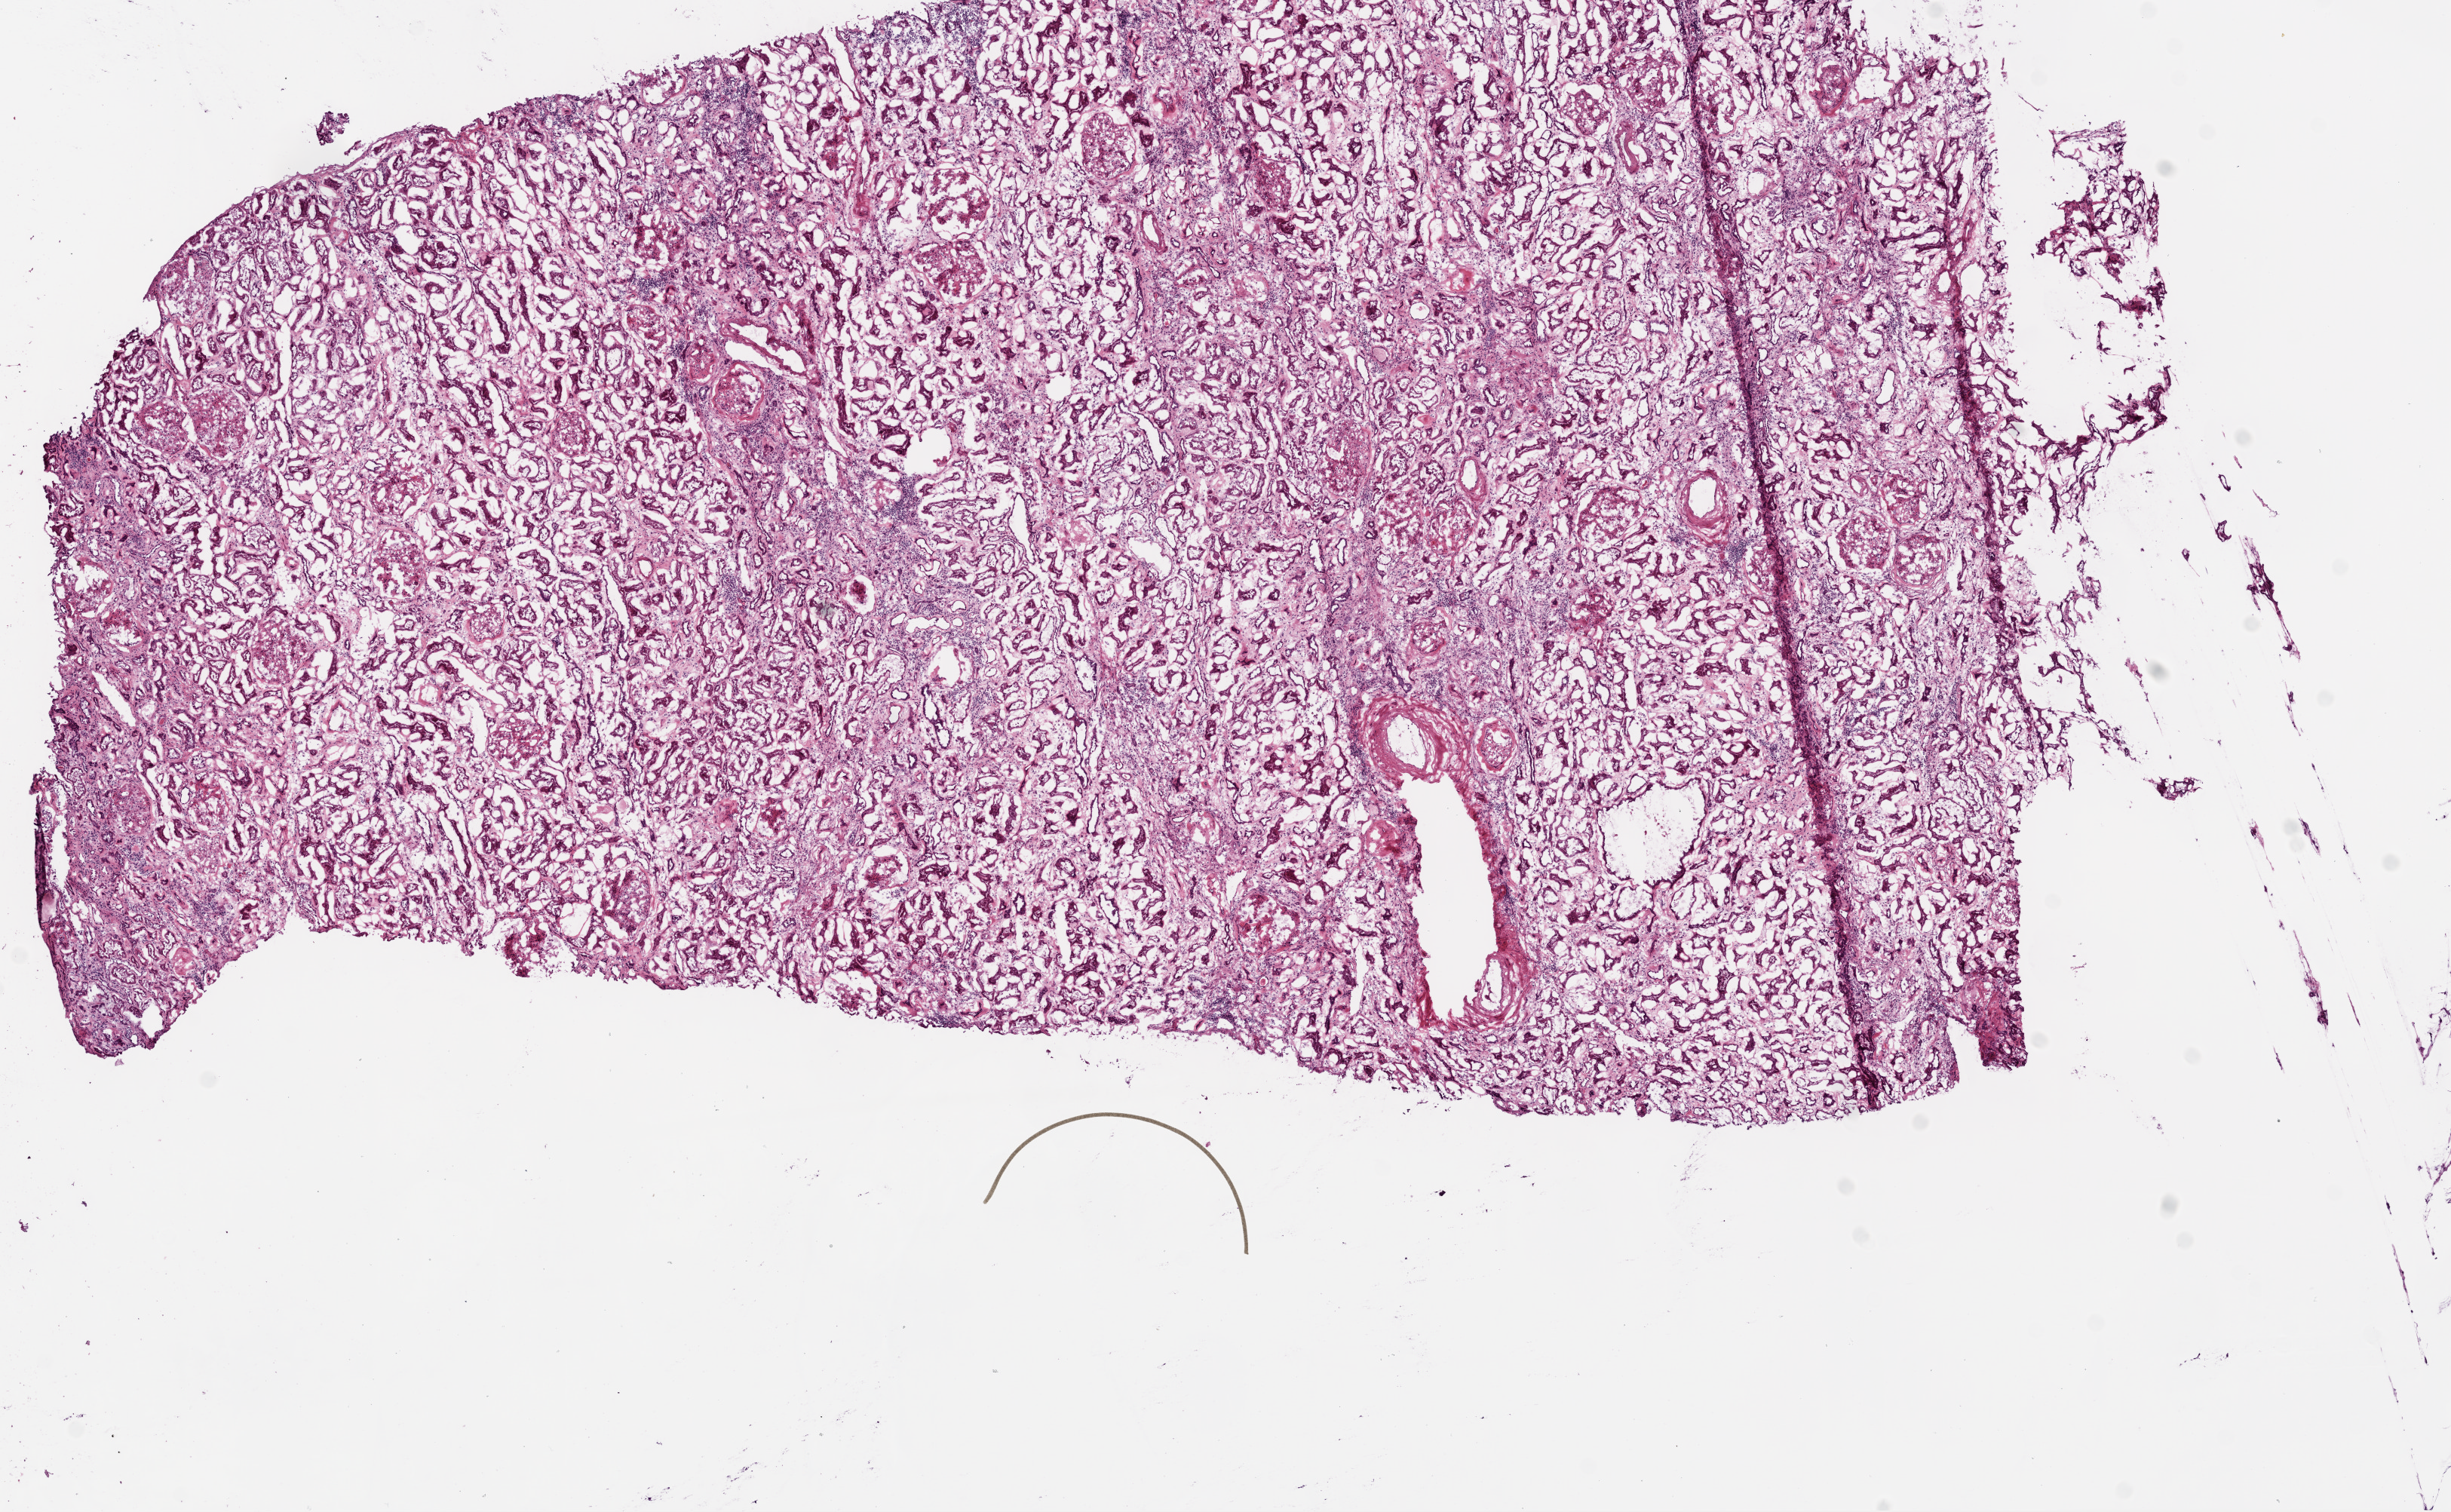
Digitized H&E-stained tissue section (whole slide), whole scanned area (about 13.0 x 8.0 mm, from a 20x scan) shown as a low-resolution overview; frozen section; kidney, solid tissue normal (non-tumour tissue) sample. Male, age 57 years at initial diagnosis.
* this section: solid tissue normal sample (biorepository sample class)
* patient diagnosis: Clear cell adenocarcinoma, NOS